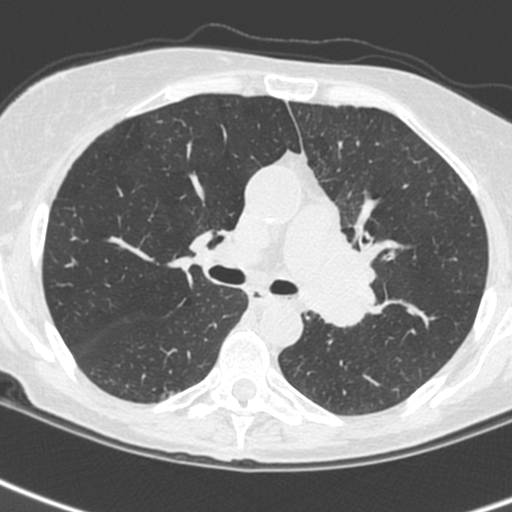
Low-dose screening chest CT, one axial slice; slice 153 of 242 in the series (ordered by position); lung window (W 1500 / L -600 HU); 1.3 mm slice thickness; 512 × 512 image matrix, field of view 284 × 284 mm.
Annotated regions visible in this slice (outlined manually by an expert reader):
- lesion 3 (tumor, upper lobe of left lung): bounding box <311,206,377,327> (left, top, right, bottom; pixels)